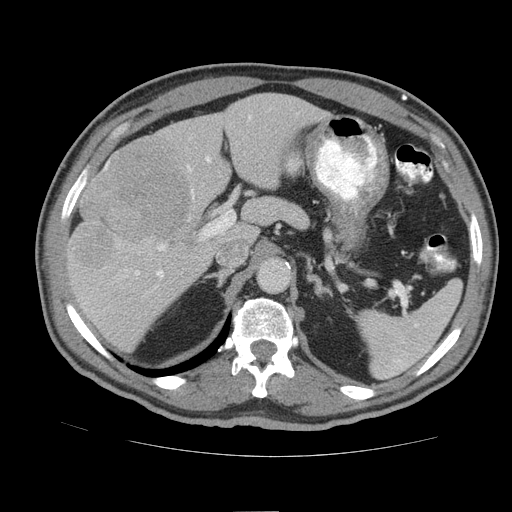
Contrast-enhanced abdominal CT (liver protocol), one axial slice; slice 57 of 105 in the series (ordered by position); reconstruction kernel STANDARD; 140 kVp; soft-tissue window (W 400 / L 40 HU); 2.5 mm slice thickness; 512 × 512 image matrix, field of view 380 × 380 mm. Case-level facts recorded for this patient, not image findings: diagnosis: hepatocellular carcinoma (patient treated with transarterial chemoembolisation; whether this scan precedes or follows treatment is not stated here); TNM stage (as recorded): Stage-IIIB; Child-Pugh class: A; tumour nodularity: multinodular.
Outlined on this slice (semi-automatic segmentation, software-assisted and operator-edited):
- liver parenchyma outside the tumour (the mass and vessels are separate outlines, so this box may not span the whole liver): bounding box (x1, y1, x2, y2) in pixels: (66, 94, 330, 352)
- mass: (74, 142, 192, 268)
- liver vessels: (104, 116, 251, 278)